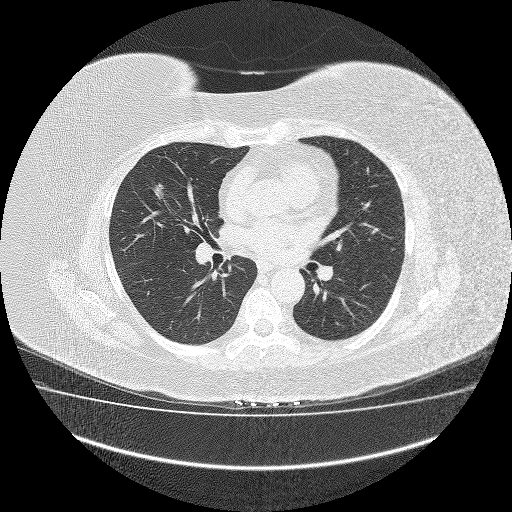
Low-dose screening chest CT, axial slice, third annual screen, lung window (W 1500 / L -600 HU), lung (sharp) reconstruction kernel (FC51). Female participant, aged 64 years at enrolment.
Expert reader's lesion annotation, bounding box [x1, y1, x2, y2] px = [127, 166, 176, 213]. Screening reader's record for this exam (one nodule recorded; not confirmed to be the boxed lesion): non-calcified nodule or mass ≥4 mm, right middle lobe, 23 × 13 mm, smooth margins, soft tissue attenuation, pre-existing on the prior screen: no. Participant outcome: lung cancer diagnosed 31 days after this screen — carcinoid tumor, NOS, right middle lobe, 3 mm at pathology.